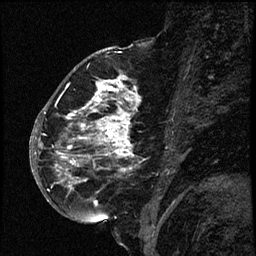
Breast MRI (dynamic contrast-enhanced), one sagittal slice; slice 33 of 66 in the series (ordered by position); dynamic contrast-enhanced study with each time point stored as its own series, time point 2 of 3 at this slice position (early post-contrast, ordered by acquisition time); 1.5 T; TE 4.2 ms, TR 17.6 ms; 2 mm slice thickness; 256 × 256 image matrix. Female patient. From the clinical record (not read from this slice): setting: breast cancer imaged before/during neoadjuvant chemotherapy; receptor status: HER2-positive.
Outlined on this slice (semi-automatic segmentation, software-assisted and operator-edited):
- analysis volume of interest (the breast-tissue region the enhancement analysis was run in; not a lesion): bounding box (x1, y1, x2, y2) in pixels: (52, 69, 153, 209)
- tumour enhancement mask (voxels above the 100 % enhancement threshold inside the analysis volume of interest): (55, 76, 139, 204)